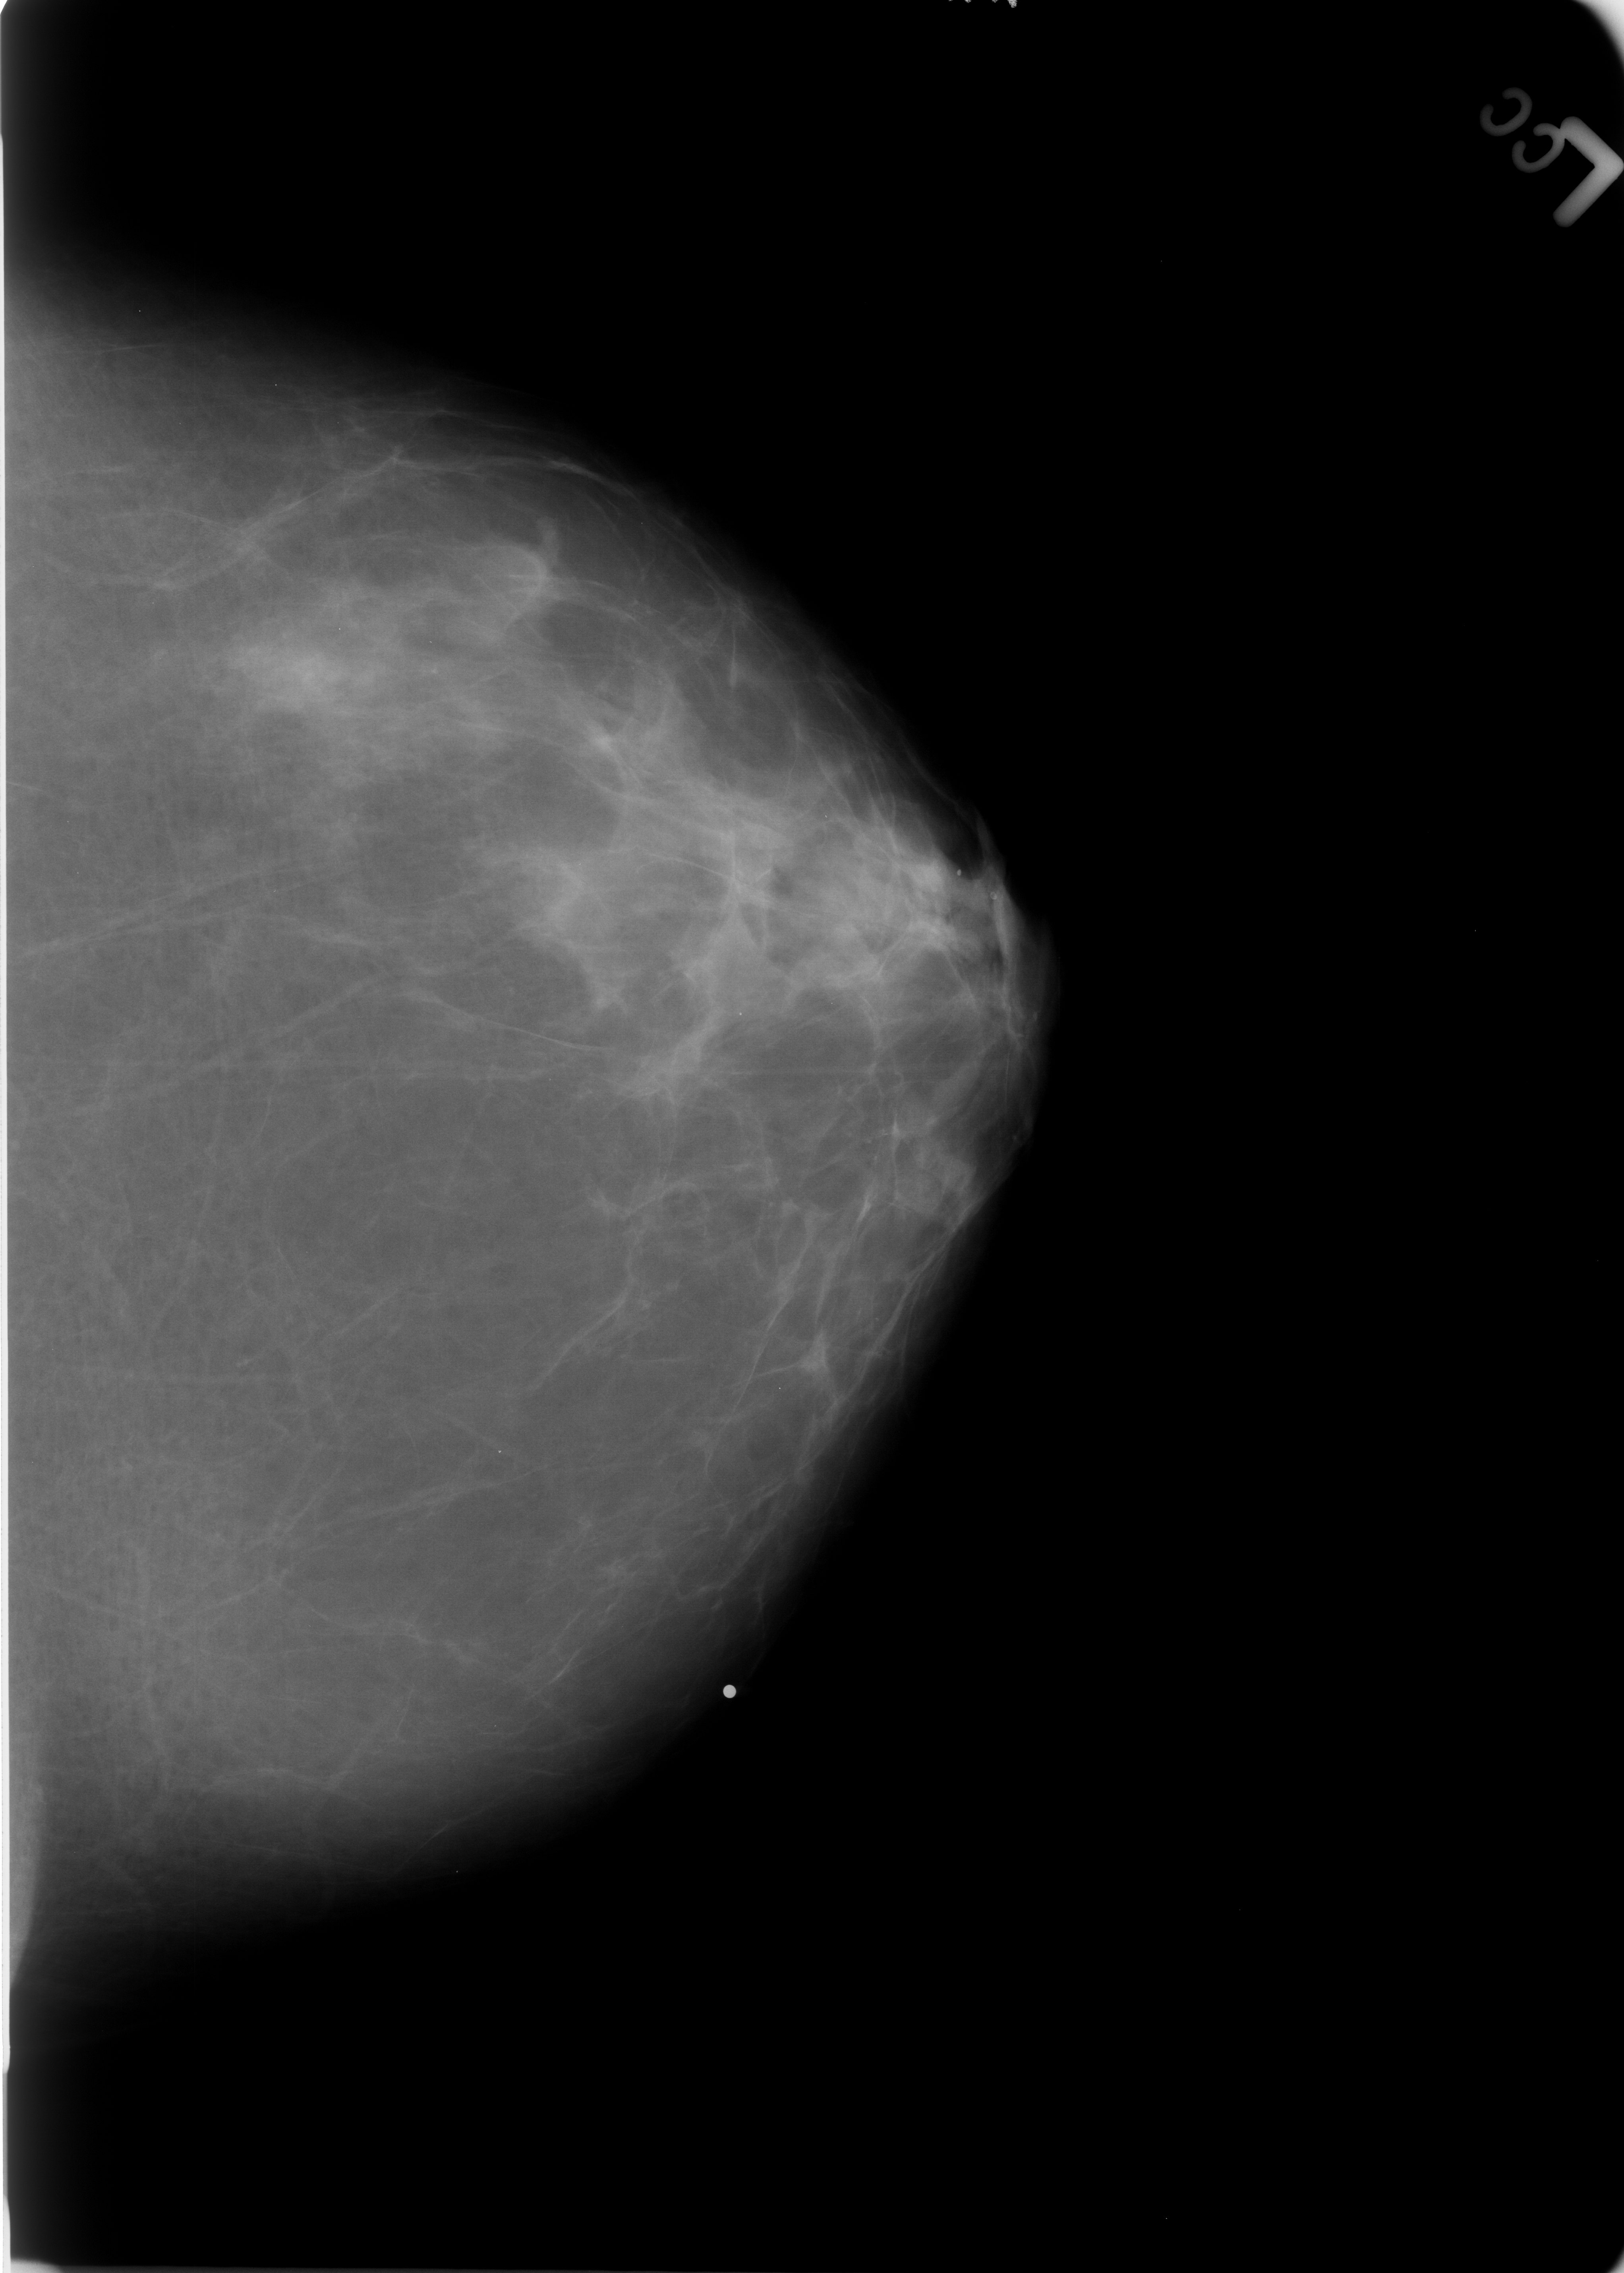
Scanned film-screen mammogram; left breast; craniocaudal (CC) view; 1624 × 2273 image matrix.
Expert-marked regions of interest on this image (one box per marked abnormality):
- Finding 1 of 2: calcifications, morphology lucent center / punctate; BI-RADS assessment category 2; outcome (as recorded, no biopsy): benign without callback (not worked up further): box from (x=931, y=851) to (x=980, y=904) px
- Finding 2 of 2: calcifications, morphology lucent center / punctate; BI-RADS assessment category 2; subtlety rating 5 on a 1 (subtle) to 5 (obvious) scale; benign; no additional work-up was recommended (outcome (as recorded, no biopsy): benign without callback): (x=975, y=877)–(x=1012, y=916)